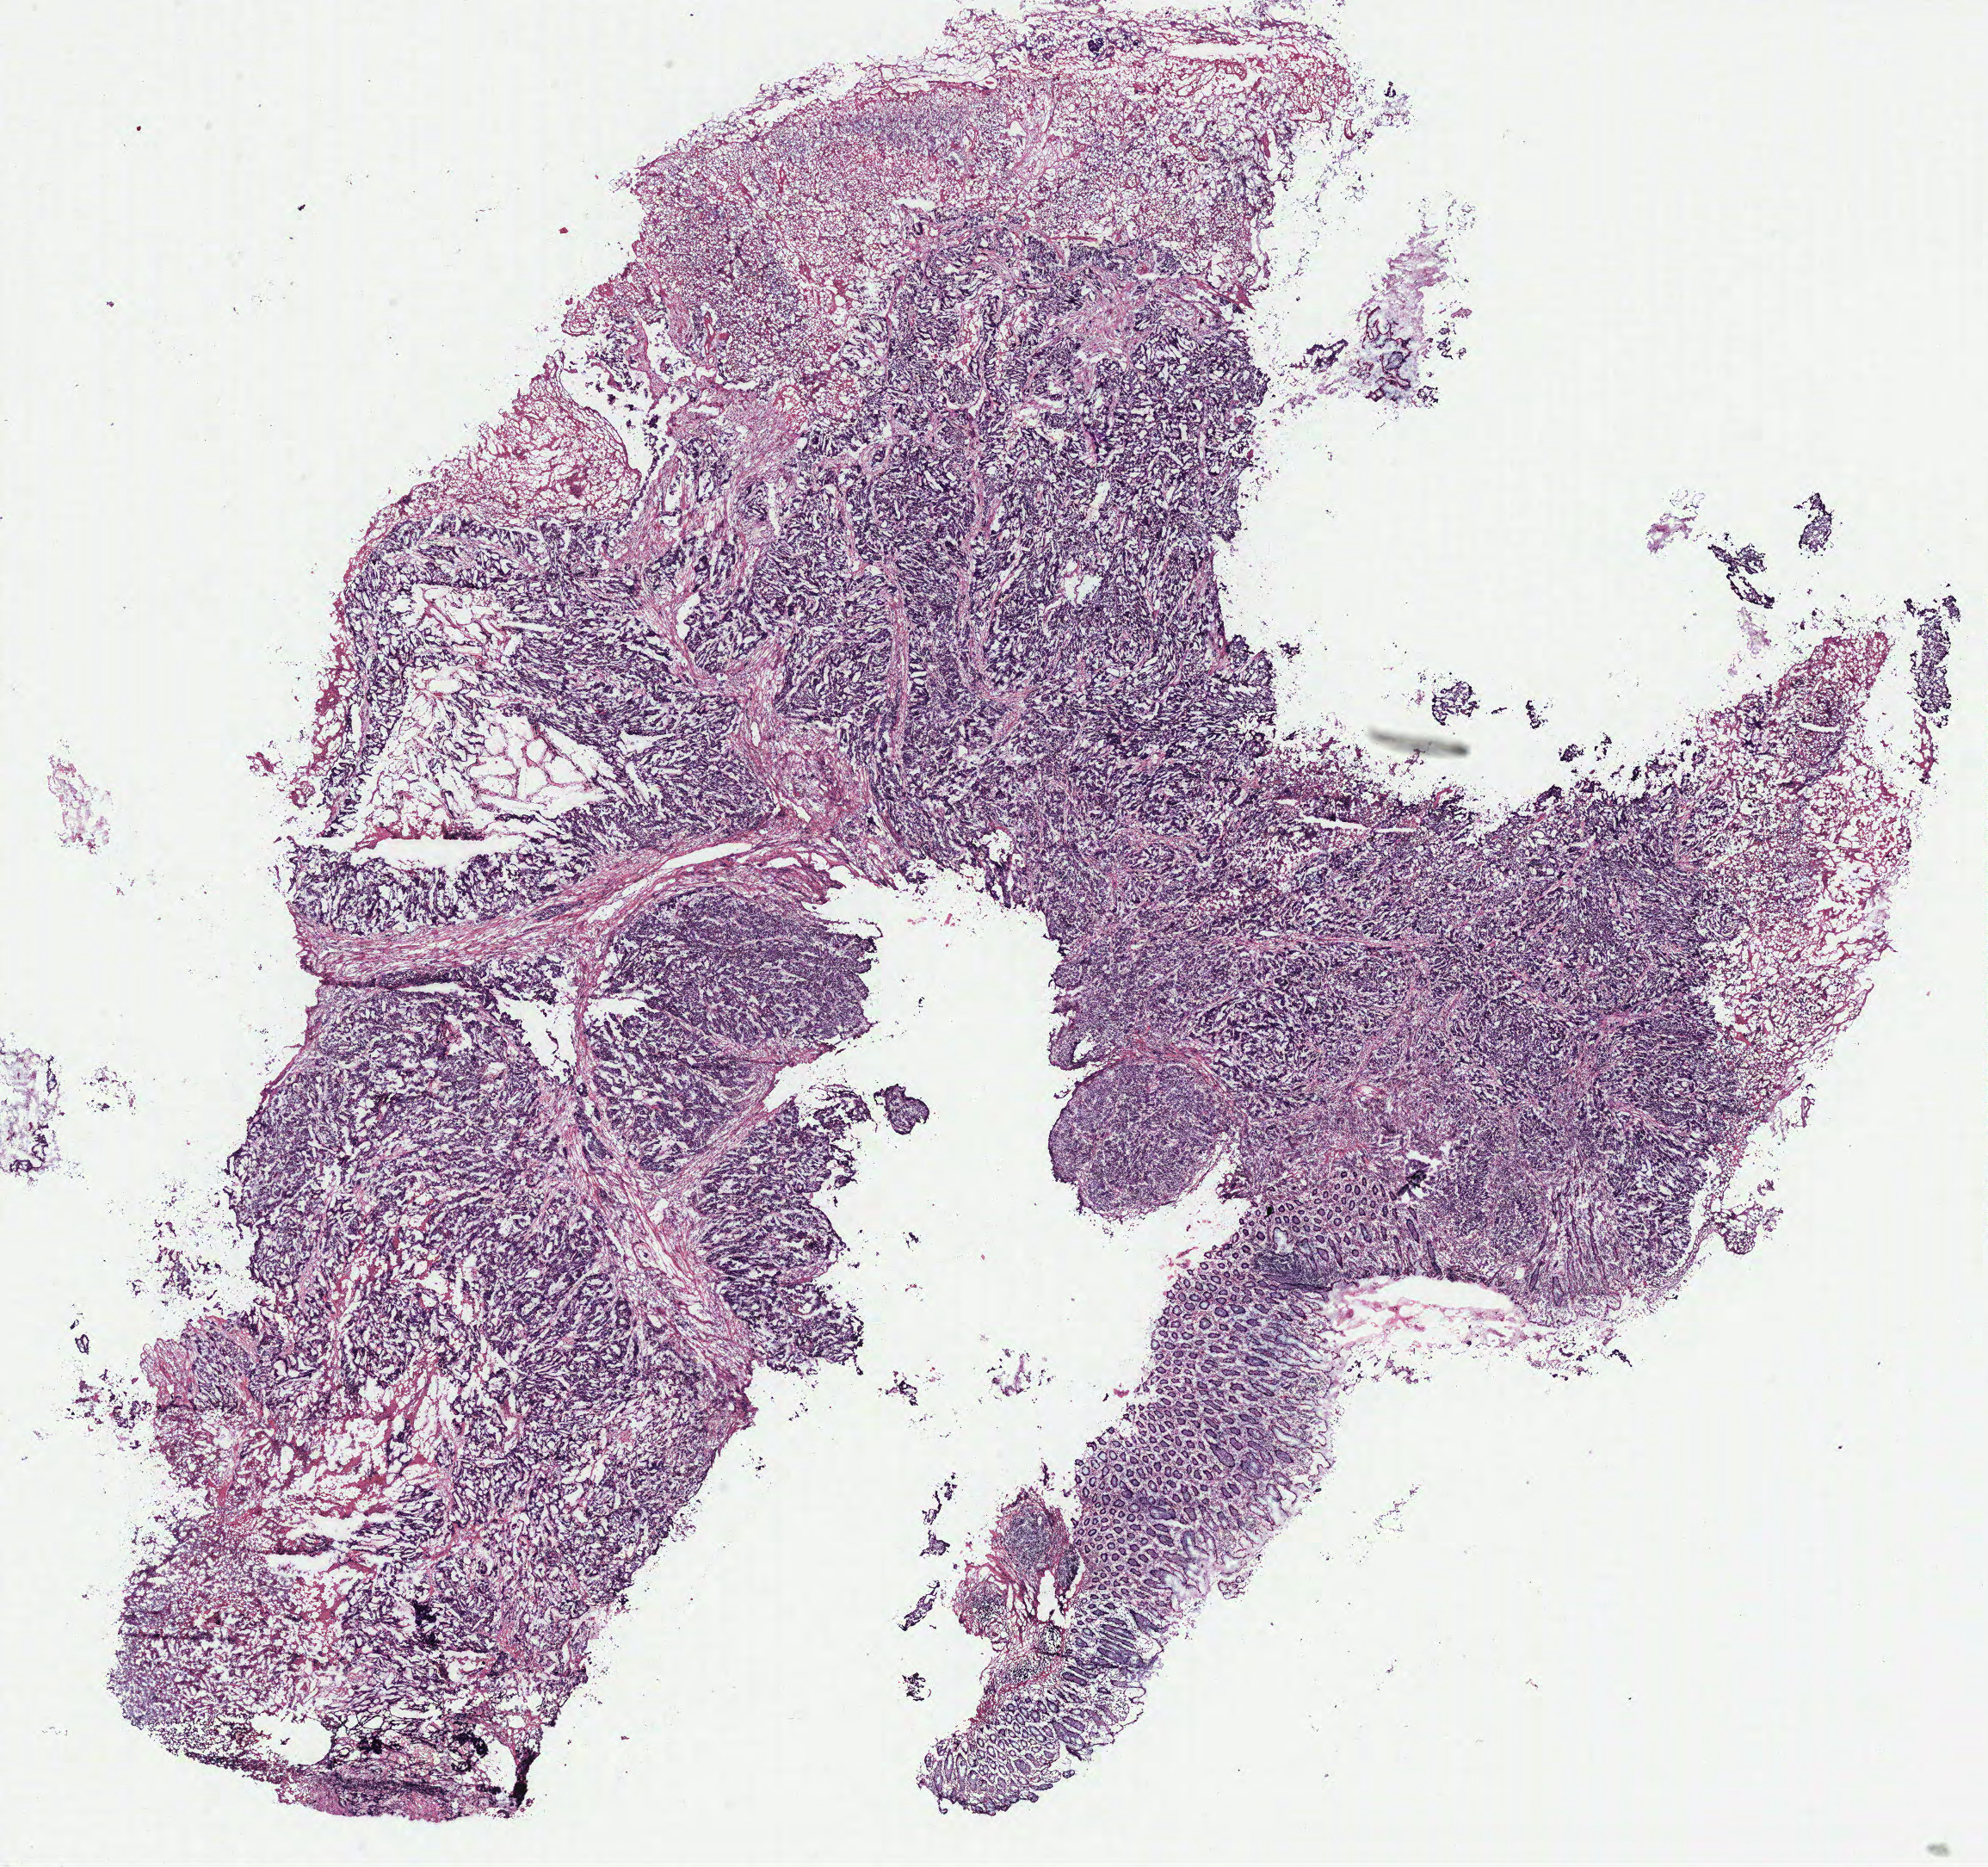
Whole-slide histology image, Hematoxylin and eosin (H&E) stained, shown as a low-resolution overview of the whole scanned area (about 18.5 x 17.4 mm, slide scanned at 40x). Tumour tissue sample, colon. 64-year-old female patient.
Primary tumour site (as recorded): colon. Diagnosis: Adenocarcinoma, NOS. AJCC pathologic stage: IIA.